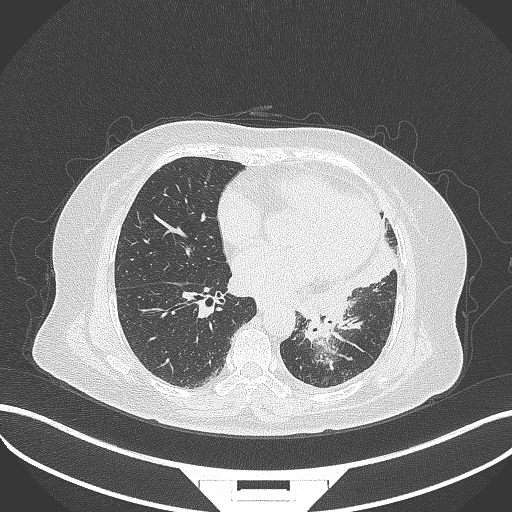
Chest CT, one axial slice; slice 148 of 322 in the series (ordered by position); 120 kVp; lung window (W 1500 / L -600 HU); 1 mm slice thickness; 512 × 512 image matrix, field of view 400 × 400 mm. Female patient, age 69 years. From the clinical record (not read from this slice): clinical TNM (as recorded): T2b N3 M1.
Outlined on this slice (rectangle marked by the reading radiologist):
- lung tumour (recorded histology: adenocarcinoma): bounding box (x1, y1, x2, y2) in pixels: (303, 312, 342, 346)